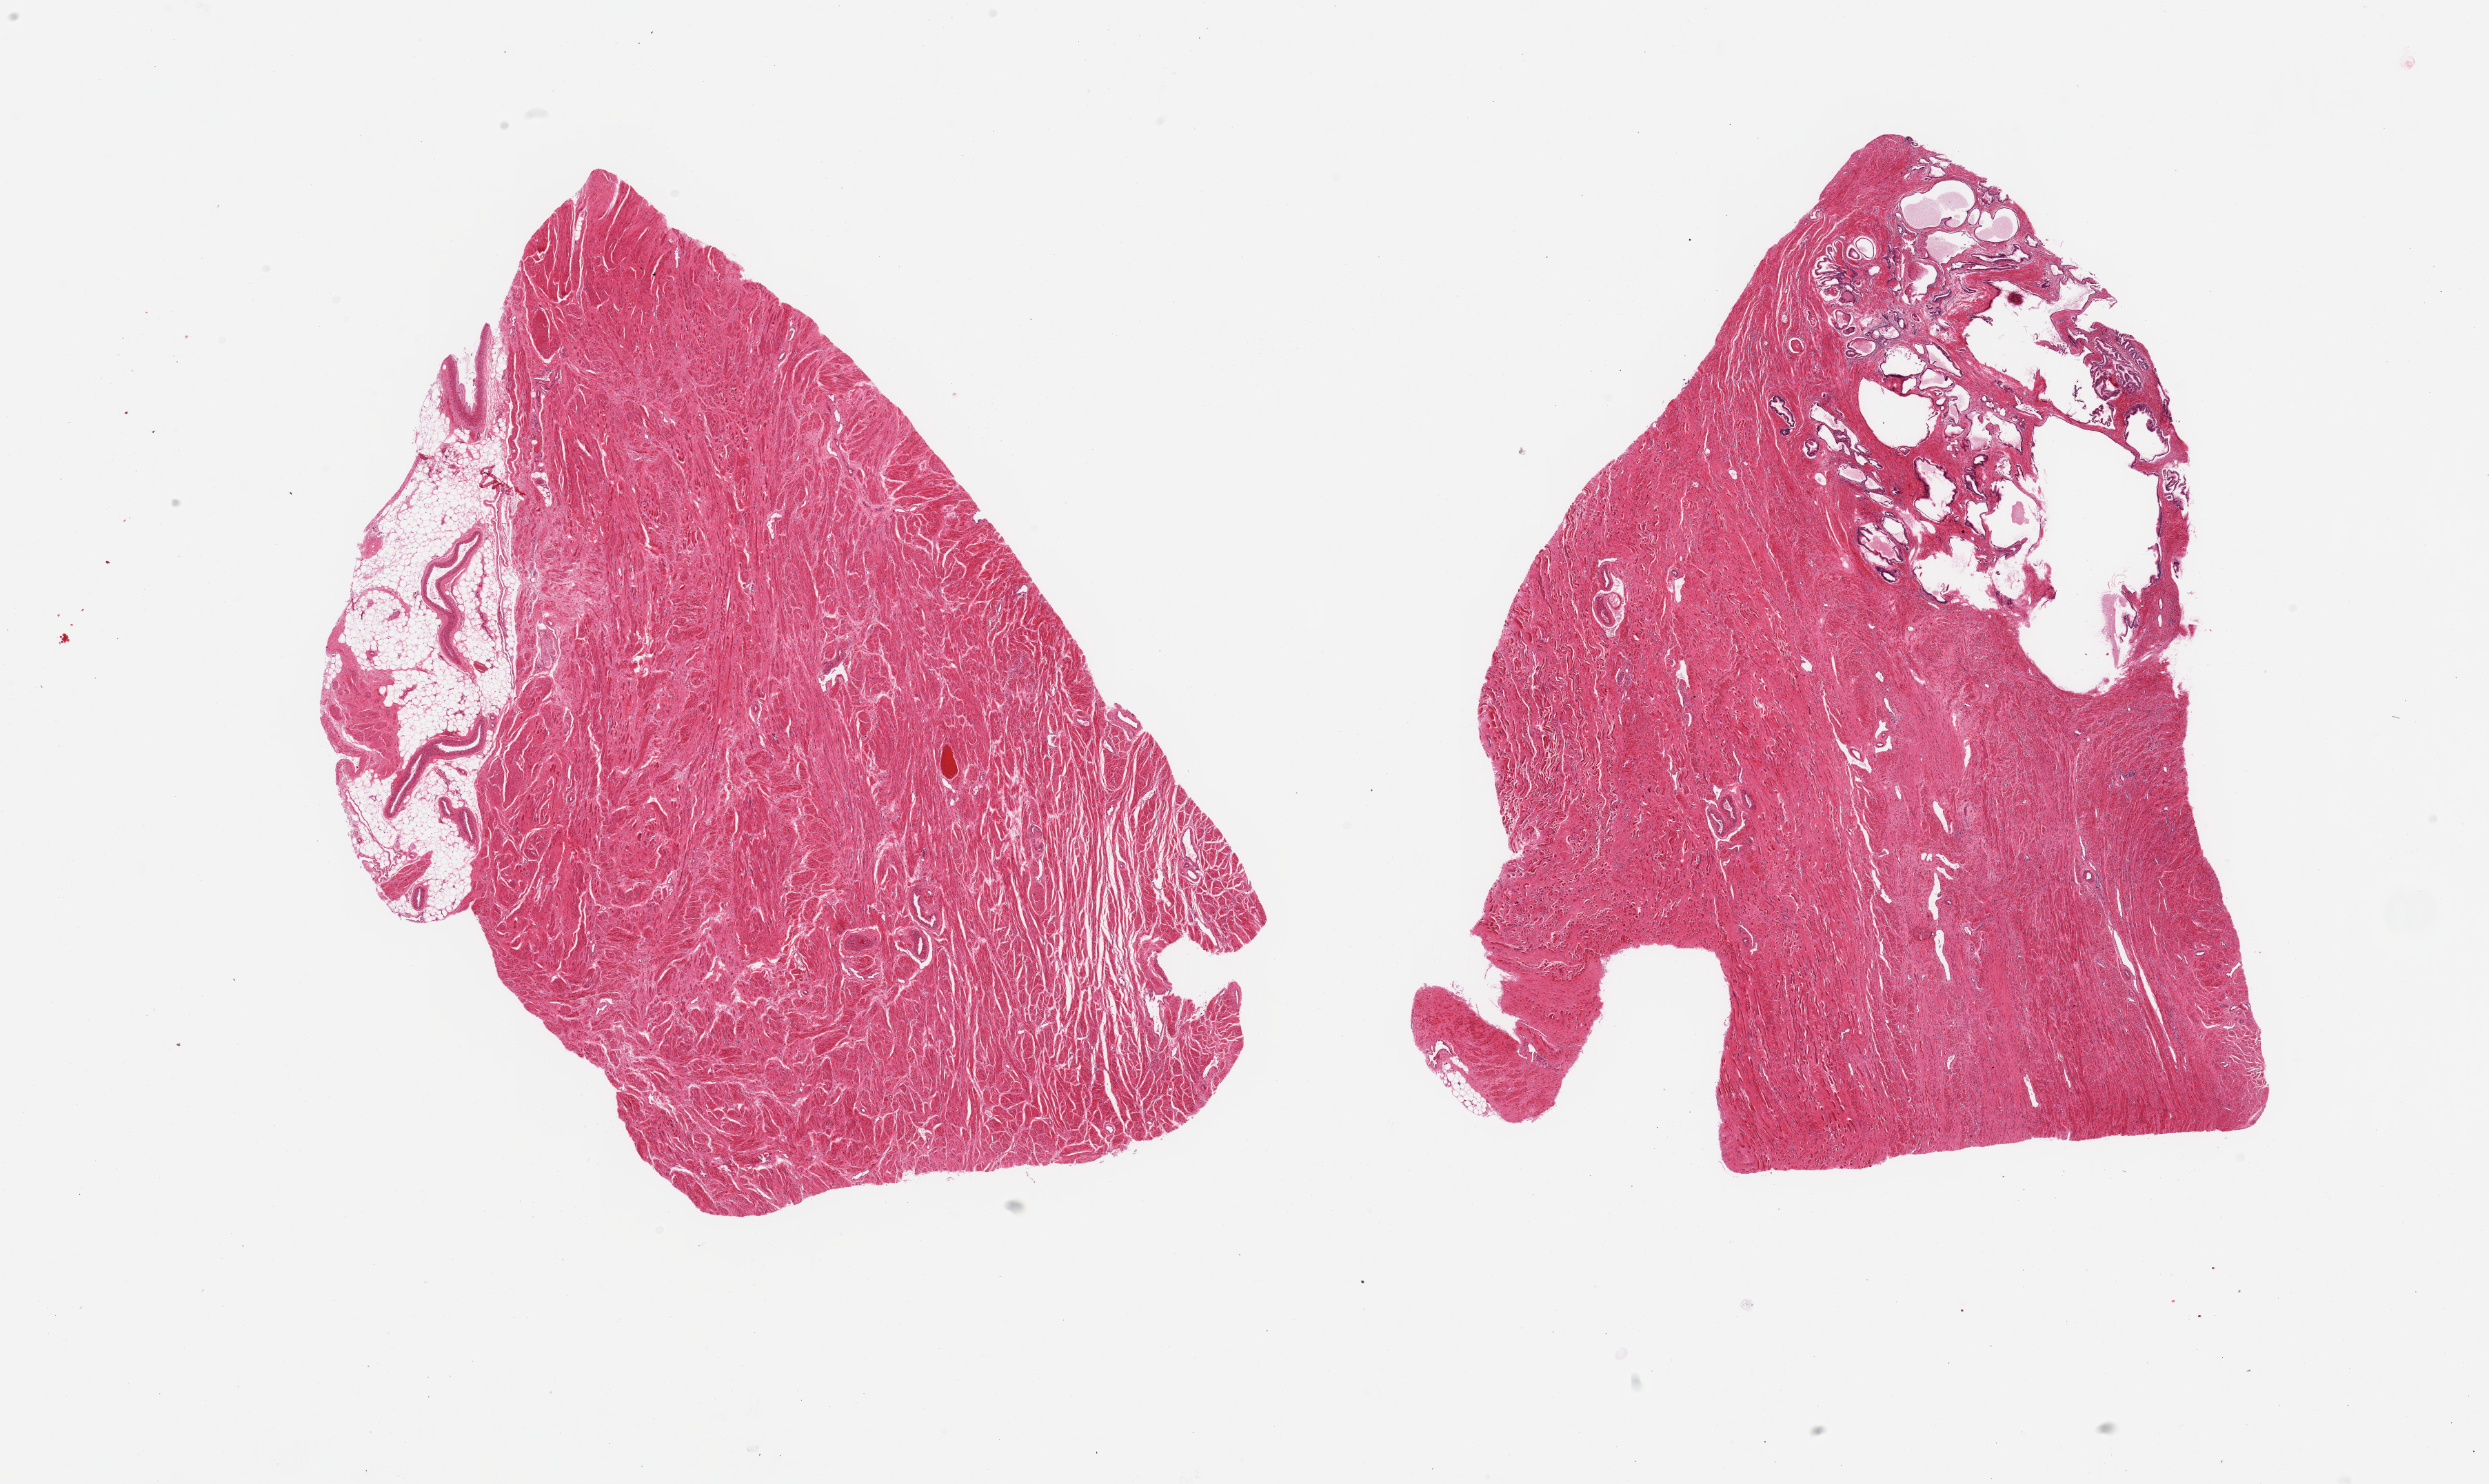
Digitized hematoxylin and eosin (H&E)-stained section, brightfield, low-resolution overview of the scanned area, about 28.5 x 17.0 mm (from a 20x scan). PAXgene-fixed paraffin-embedded (PFPE) section. Sampled site (target tissue): prostate. Tissue donor sample. Donor: male.
Pathologist's review note for this sample: 2 pieces; one with 90% fibromuscular stroma and 10% adipose tissue and other with fibromuscular stroma and moderately autolyzed glandular component with cystic dilatation.